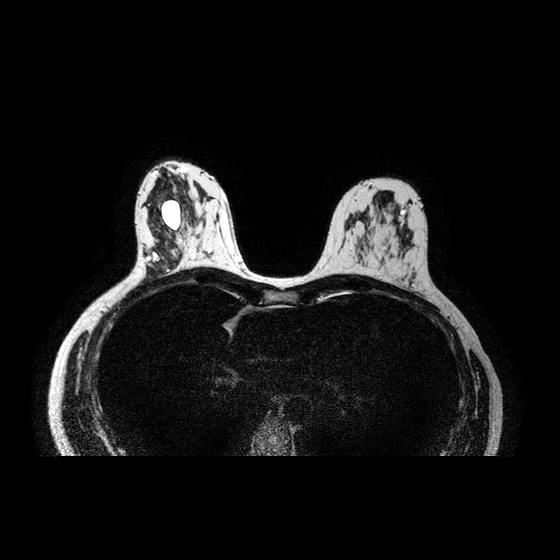
MRI of the breasts; 2 images, each one mid-volume slice chosen by position.
Image 1: axial T2-weighted / STIR image, slice 43 of 84.
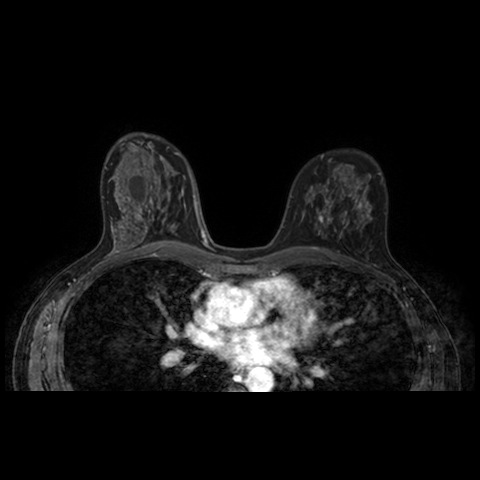
Image 2: axial dynamic contrast-enhanced T1-weighted image, series "AX BLISS_AUTO SENSE", slice 43 of 84, dynamic phase 5 of 8, 4 mm slice thickness.
Pathology recorded for this patient (not read from these images): pathology diagnosis: benign fibrosis (left breast).